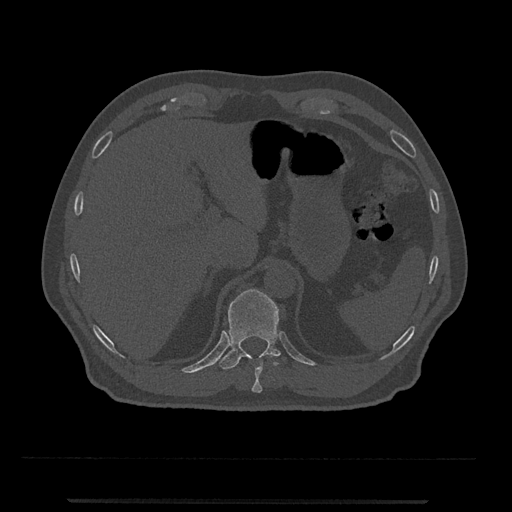
CT including the spine, one axial slice; position 481 of 797 along the scan axis; 120 kVp; bone window (W 1800 / L 400 HU); 0.5 mm slice thickness; 512 × 512 image matrix. Male patient, age 63 years. Case-level facts recorded for this patient, not image findings: primary cancer: prostate.
Structures marked on this image (semi-automatic segmentation, software-assisted and operator-edited):
- T10 vertebra: box from (x=252, y=354) to (x=278, y=393) px
- T11 vertebra: (x=218, y=289)–(x=281, y=370)